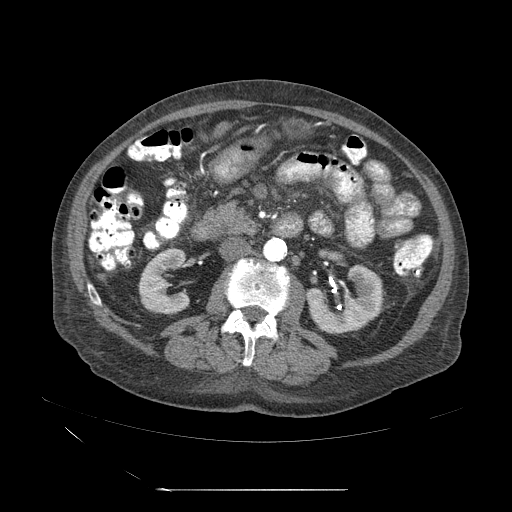
Contrast-enhanced abdominal CT (liver protocol), one axial slice; slice 5 of 71 in the series (ordered by position); reconstruction kernel STANDARD; 120 kVp; soft-tissue window (W 400 / L 40 HU); 512 × 512 image matrix, field of view 440 × 440 mm. Case-level facts recorded for this patient, not image findings: diagnosis: hepatocellular carcinoma (patient treated with transarterial chemoembolisation; whether this scan precedes or follows treatment is not stated here); TNM stage (as recorded): Stage-II; Child-Pugh class: A; tumour nodularity: multinodular; tumour size: 1 cm.
Outlined on this slice (semi-automatic segmentation, software-assisted and operator-edited):
- abdominal aorta: bounding box [x1, y1, x2, y2] px = [264, 238, 286, 264]